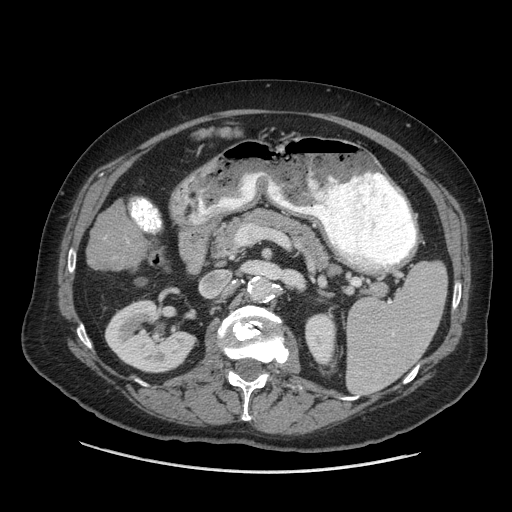
Contrast-enhanced abdominal CT (liver protocol), one axial slice; slice 23 of 77 in the series (ordered by position); reconstruction kernel STANDARD; soft-tissue window (W 400 / L 40 HU); 2.5 mm slice thickness; 512 × 512 image matrix, field of view 420 × 420 mm. From the clinical record (not read from this slice): diagnosis: hepatocellular carcinoma (patient treated with transarterial chemoembolisation; whether this scan precedes or follows treatment is not stated here); TNM stage (as recorded): Stage-I; Child-Pugh class: A; tumour size: 3.8 cm.
Outlined on this slice (semi-automatic segmentation, software-assisted and operator-edited):
- liver parenchyma outside the tumour (the mass and vessels are separate outlines, so this box may not span the whole liver): bounding box <90,200,146,260> (left, top, right, bottom; pixels)